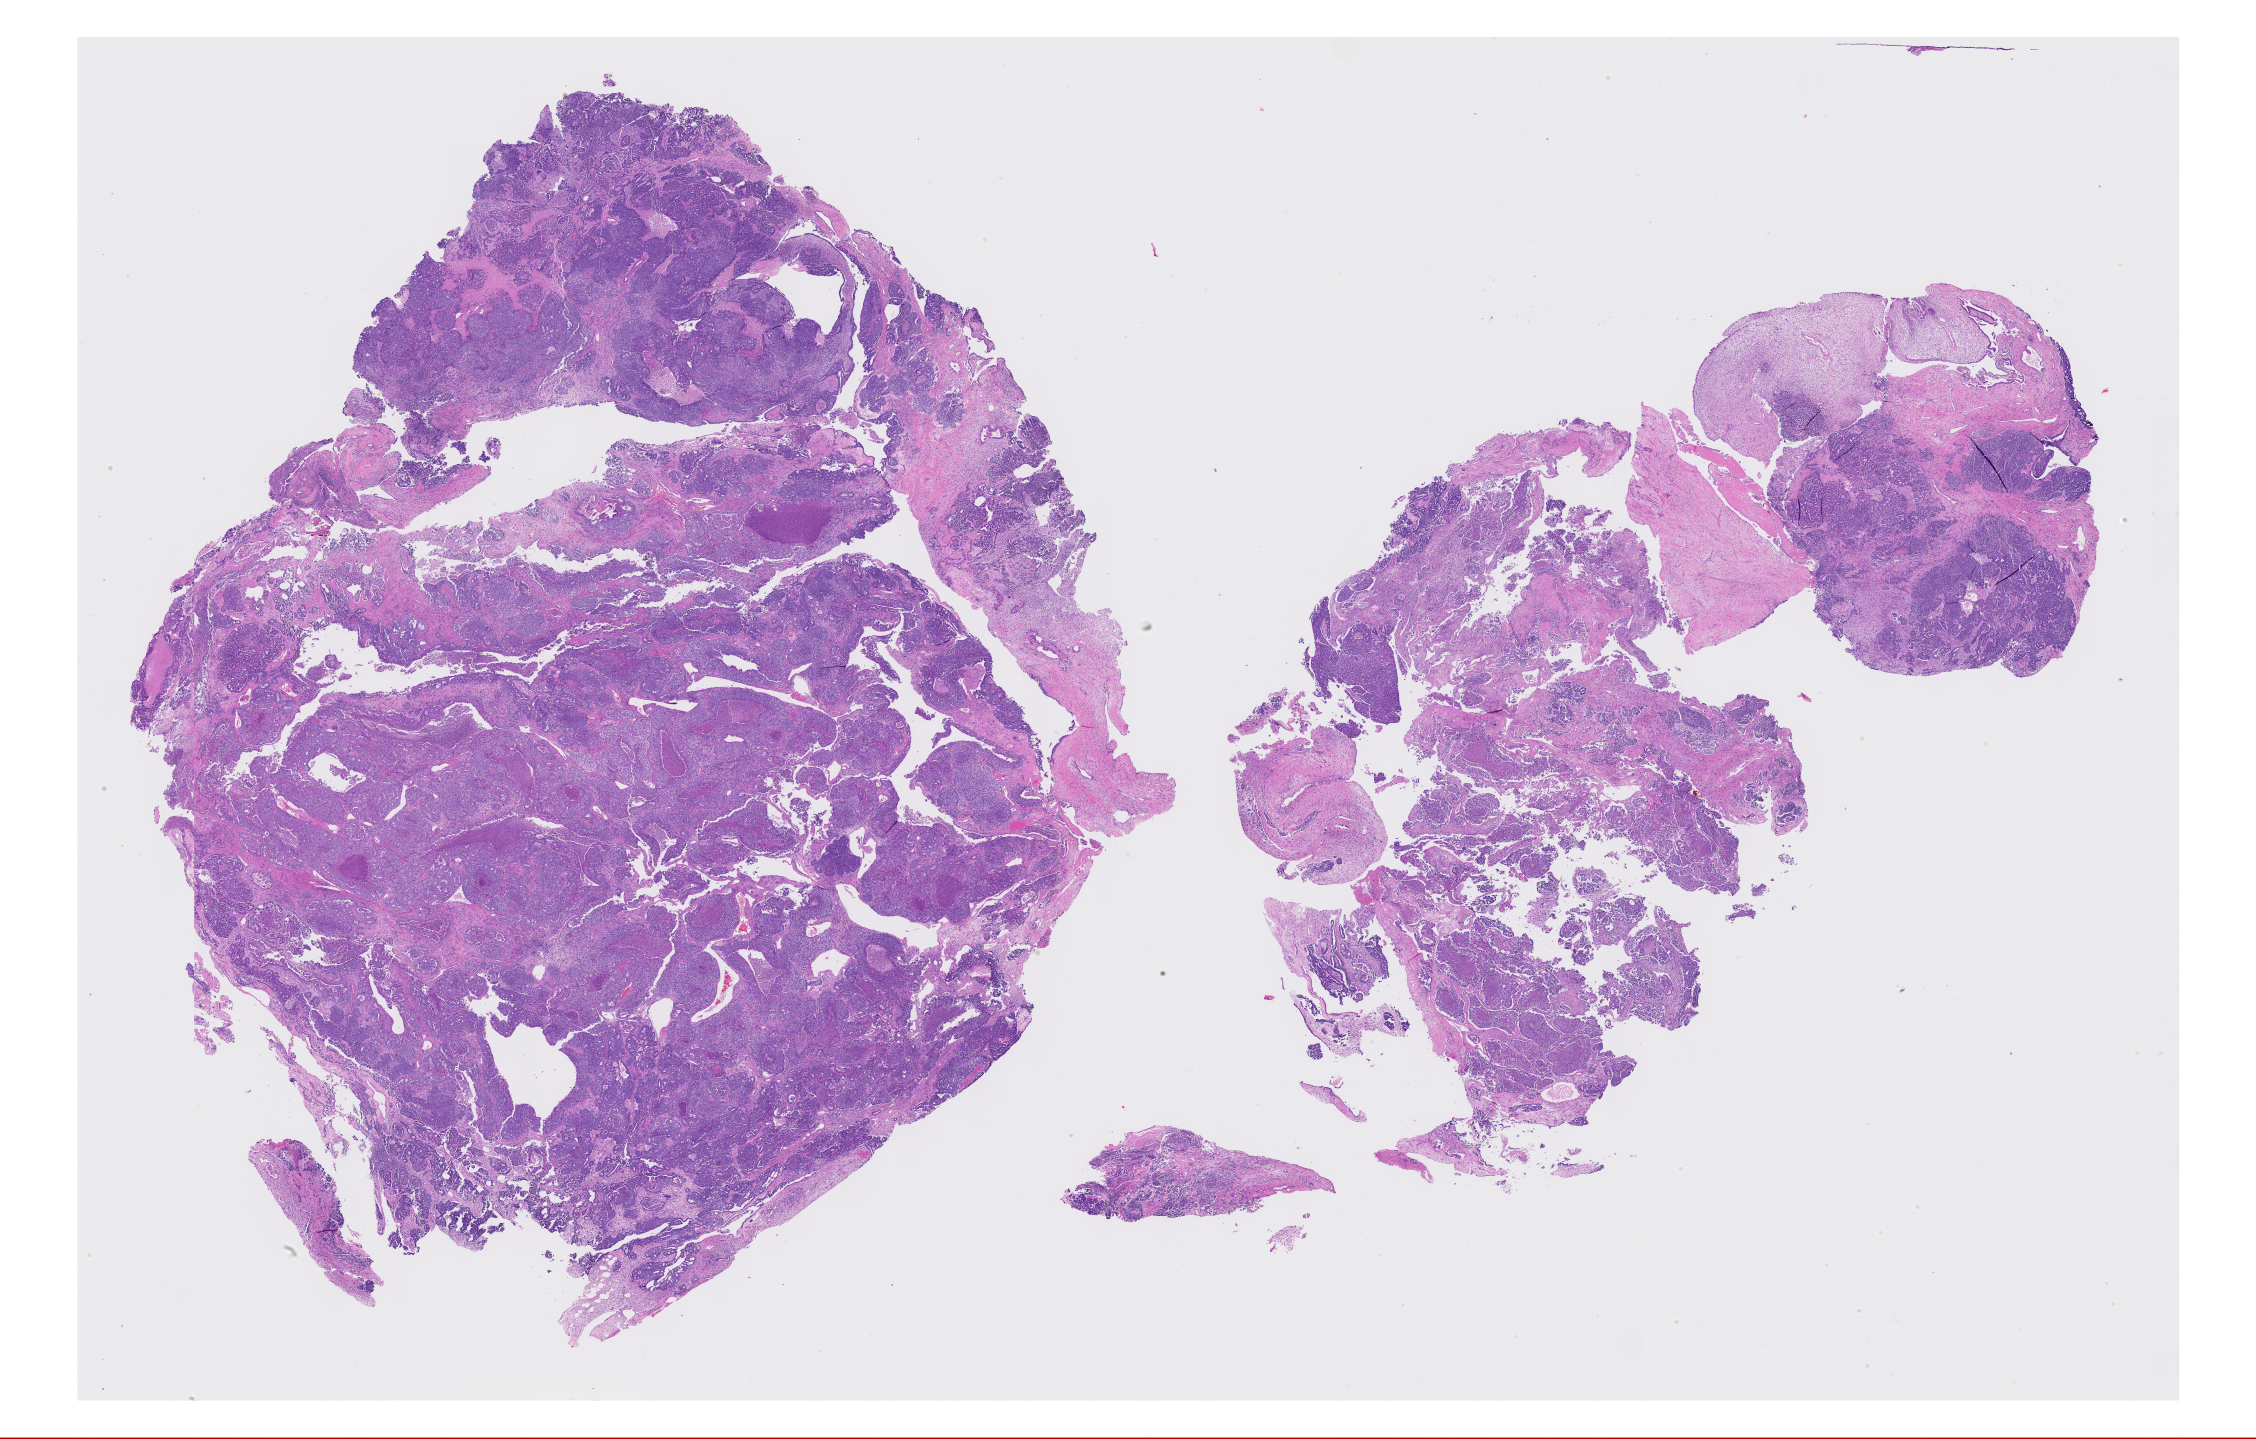
Whole-slide histology image, H&E — a low-resolution overview of the entire scanned area, about 36.1 x 23.0 mm (slide scanned at 20x), formalin-fixed paraffin-embedded (FFPE) diagnostic section, uterus, primary tumour sample. Patient: female, age at initial diagnosis 59 years.
* FIGO stage: IA
* diagnosis: Carcinosarcoma, NOS